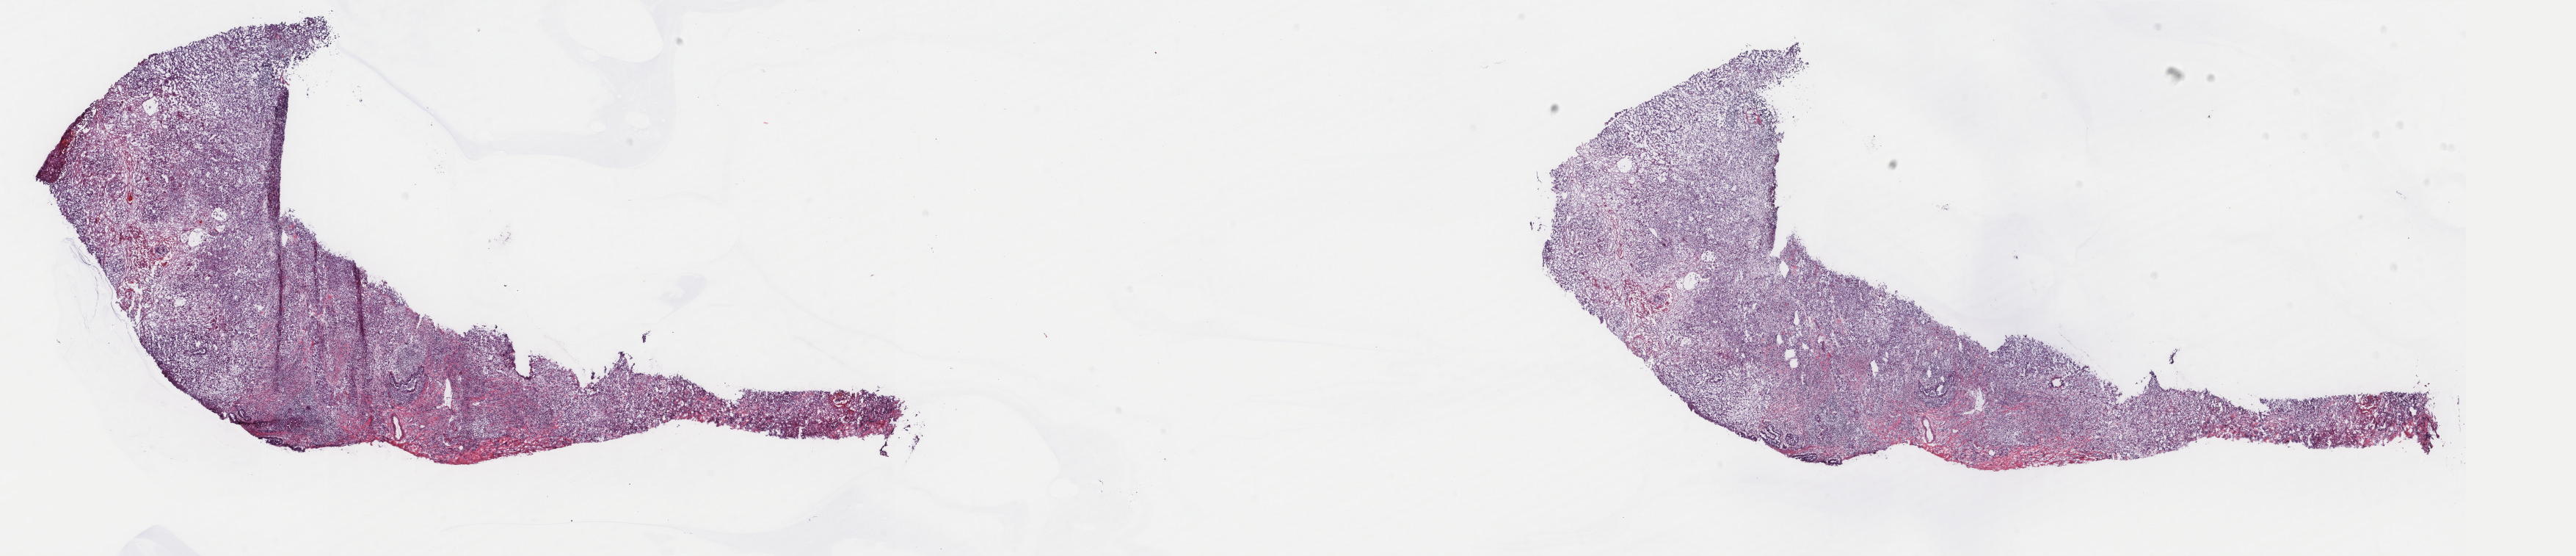
Digitized H&E-stained tissue section (whole slide), a low-resolution overview of the entire scanned area, about 27.9 x 6.0 mm (acquisition: 40x scan). Frozen section from the top of the tissue portion. Breast, primary tumour sample. Female patient; age at initial diagnosis 68 years. Pathologist review of this section (percent, as recorded): tumour cells 90%, tumour nuclei 90%, normal cells 0%, stromal cells 5%, necrosis 5%. Infiltration values recorded for this section: lymphocyte infiltration 40%, monocyte infiltration 20%, neutrophil infiltration 20%.
Diagnosis: Metaplastic carcinoma, NOS. AJCC pathologic stage: IIIA. Lymph nodes positive (case pathology): 1 of 24 examined.